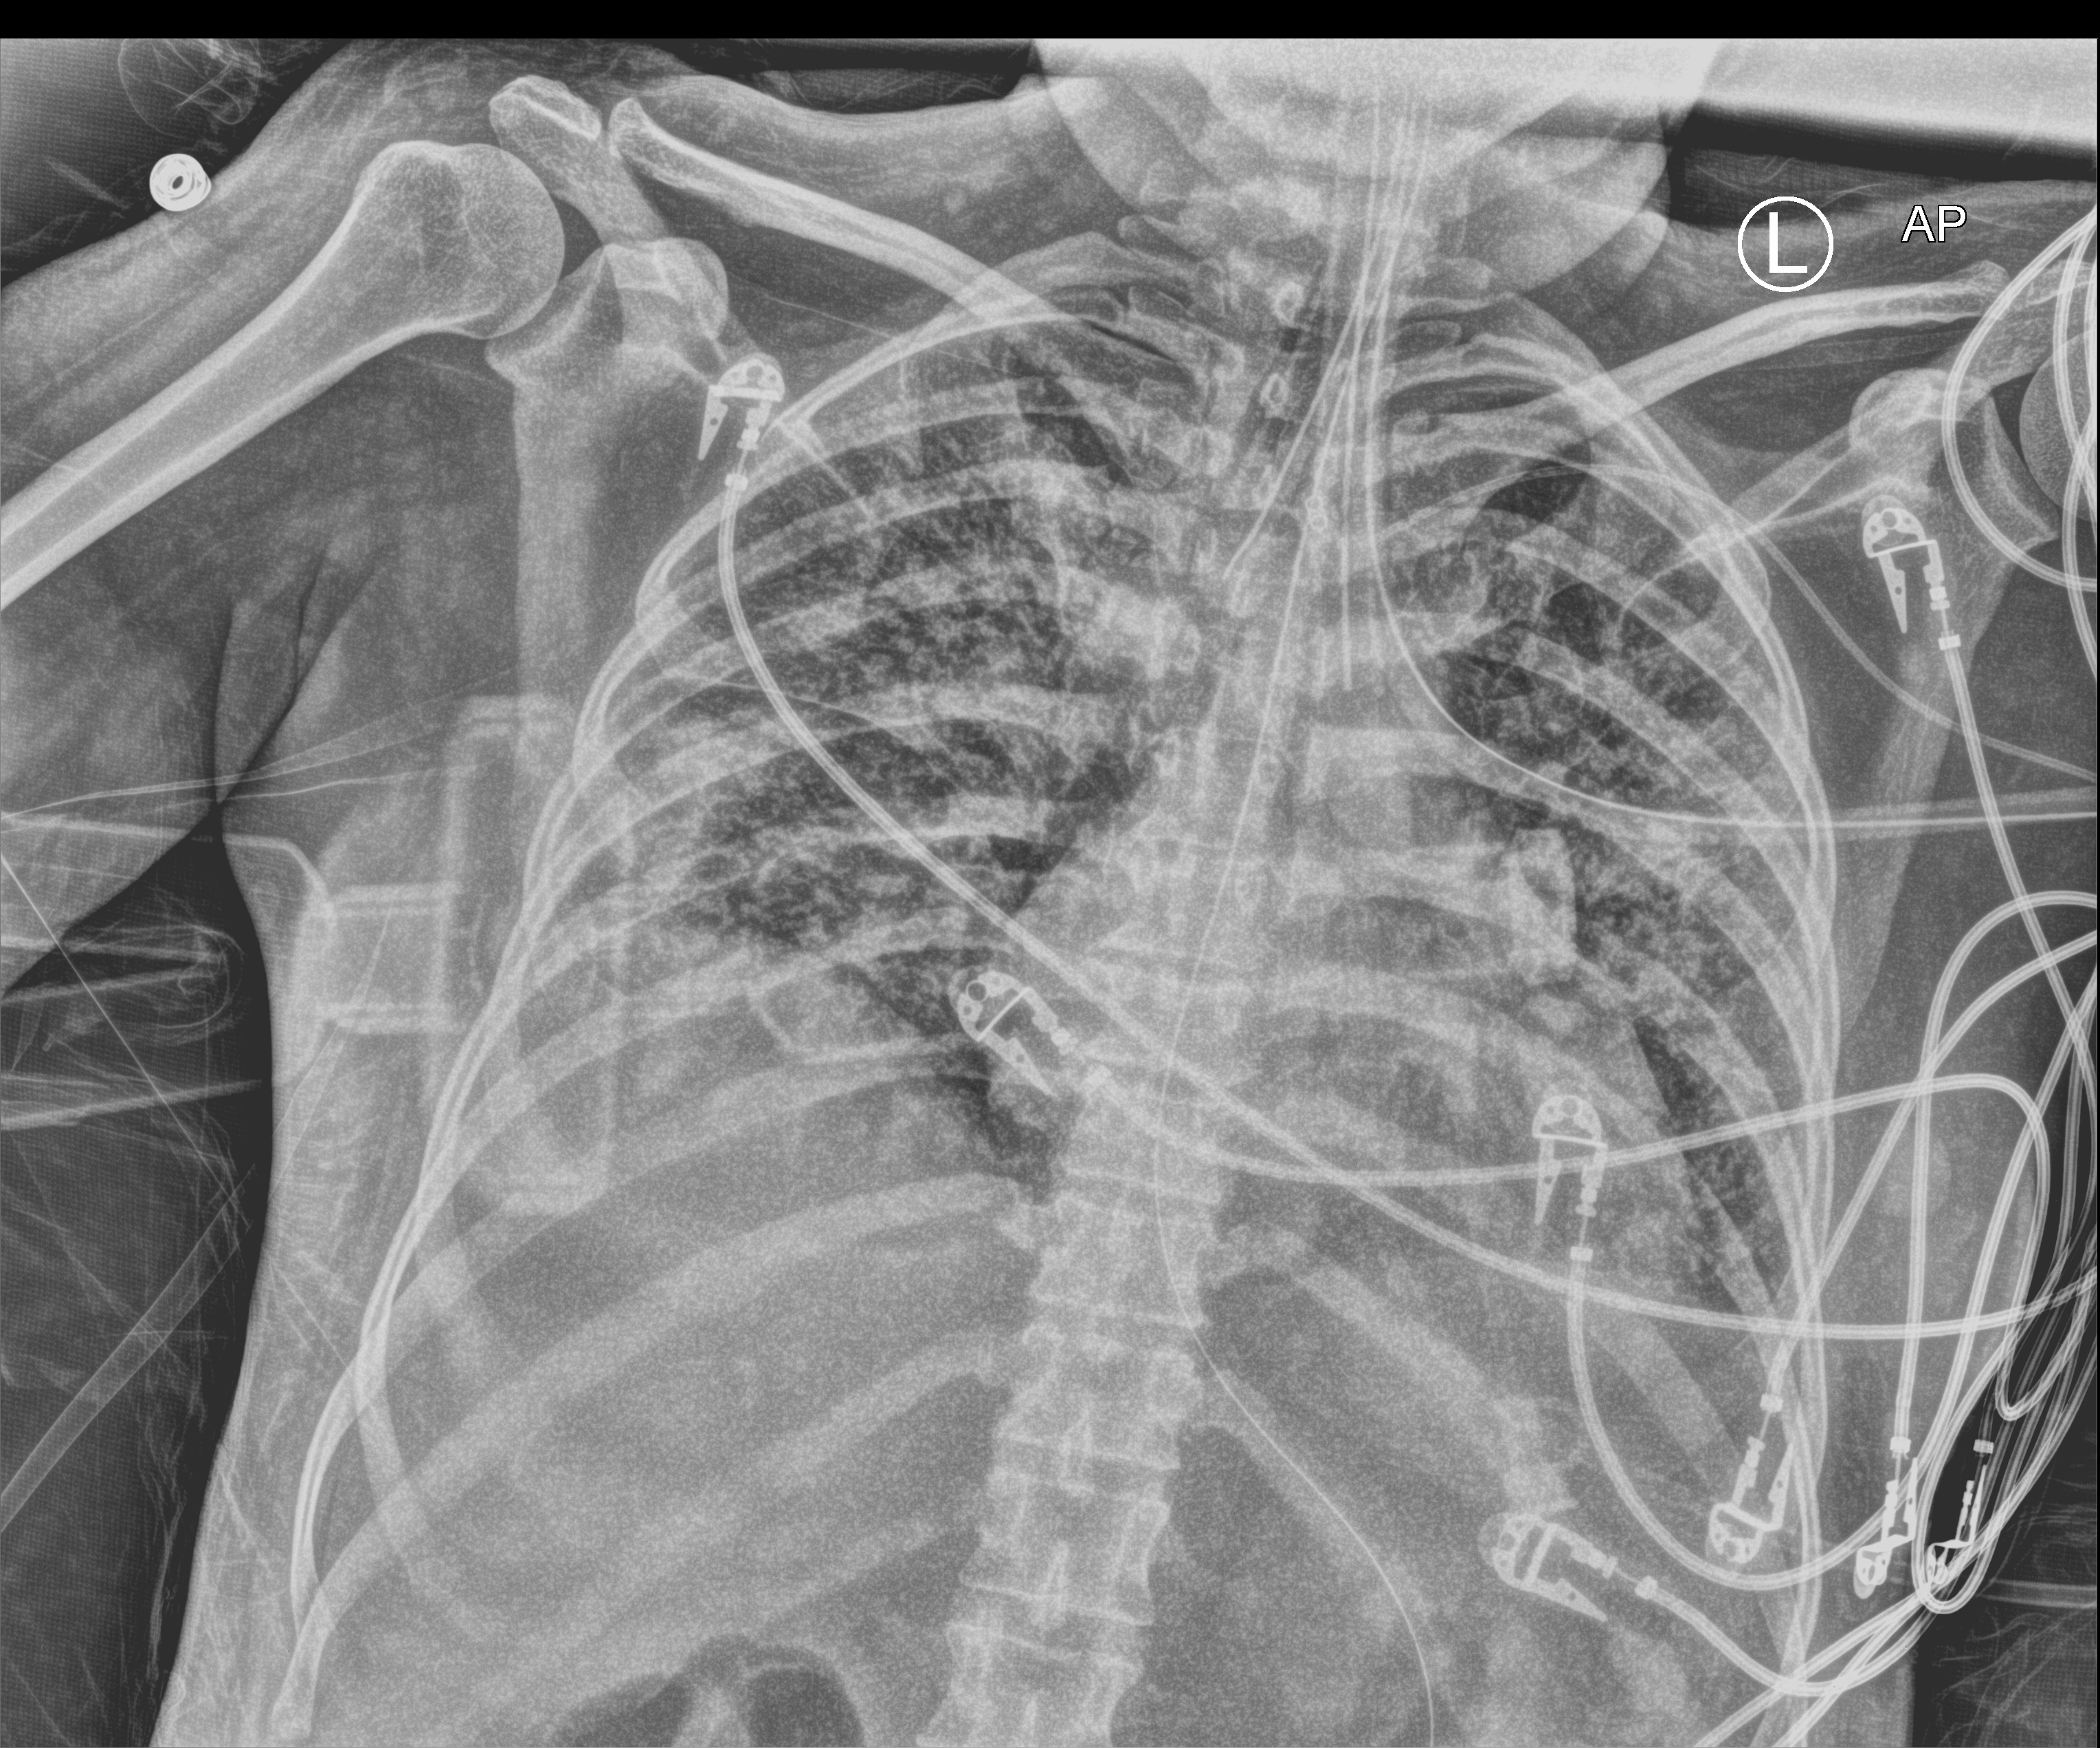
Bedside chest radiograph (computed radiography). Patient hospitalised with COVID-19; female, aged 18–59 years.
Hospital-stay facts (about this admission, not read from this image; timing relative to this image not recorded): hypertension (admission record): no; admitted to intensive care during this hospital stay: yes.